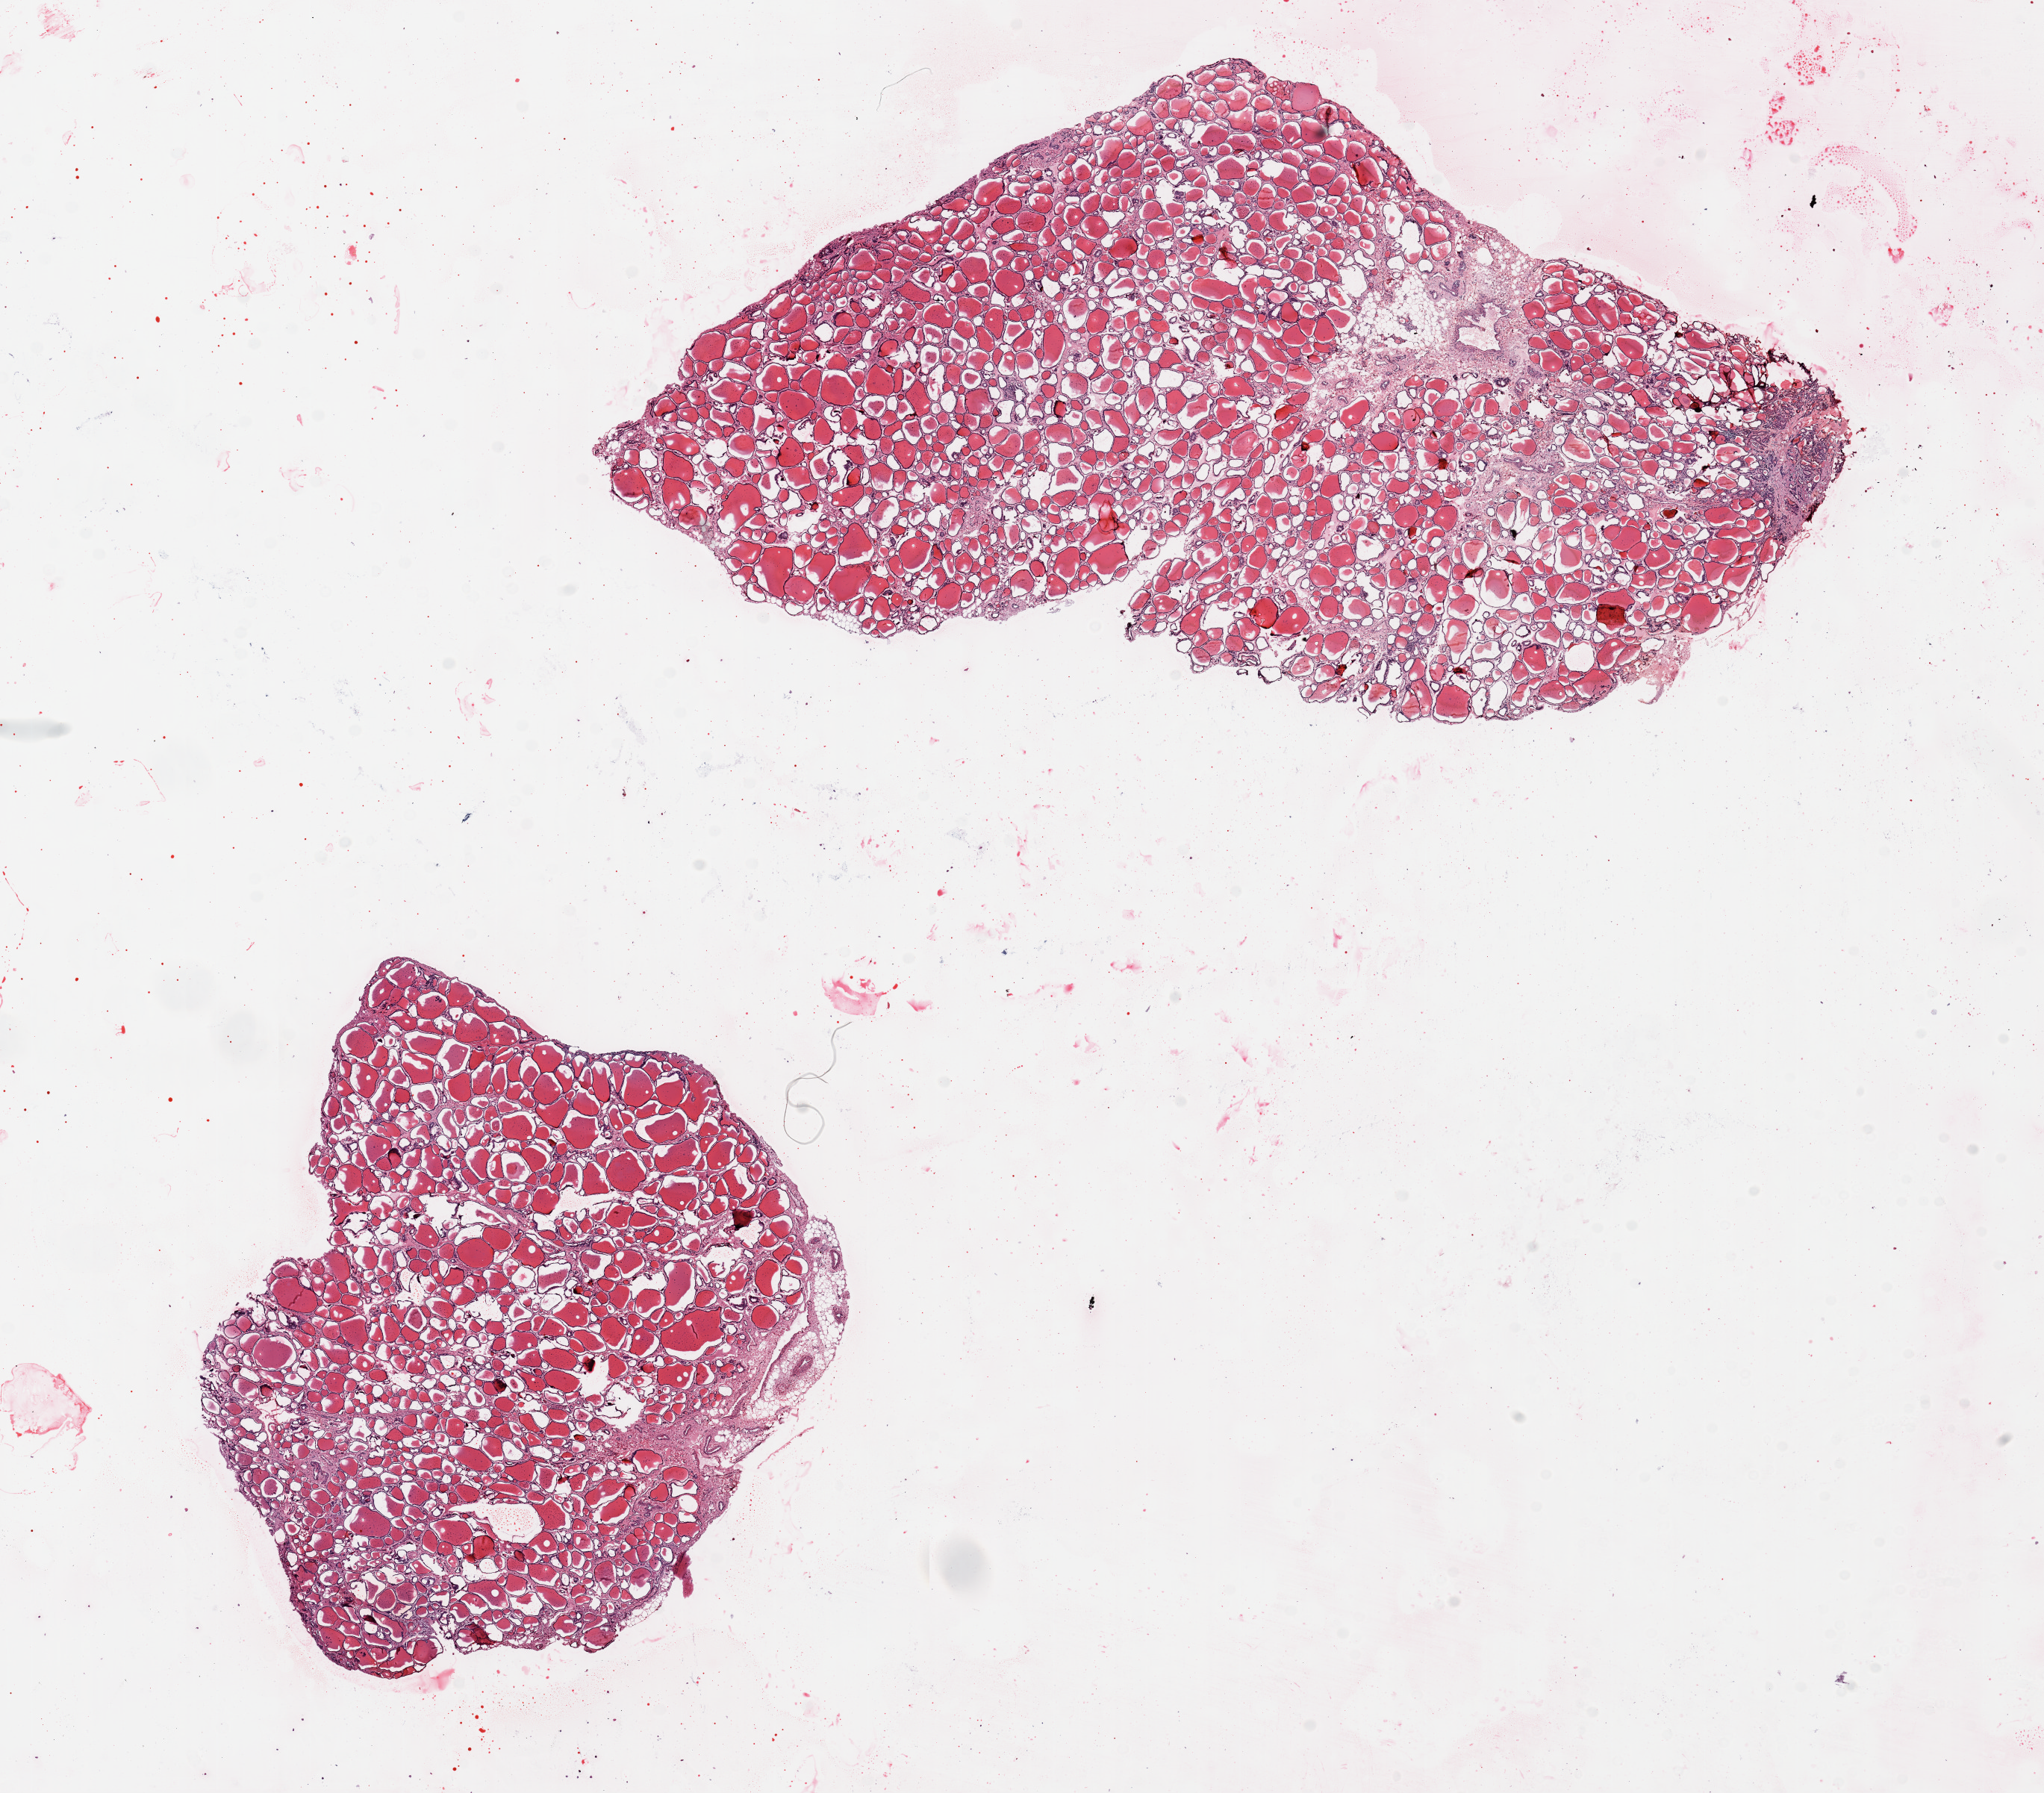
Hematoxylin and eosin (H&E) whole-slide image, a low-resolution overview of the entire scanned area, about 21.7 x 19.0 mm. PAXgene-fixed paraffin-embedded (PFPE) section. Target tissue: thyroid. Tissue donor sample.
Reviewer comment on this tissue sample: 2 pieces ~9x6mm; Incidental papillary carcinoma 1.7x1mm on one edge of one aliquot.